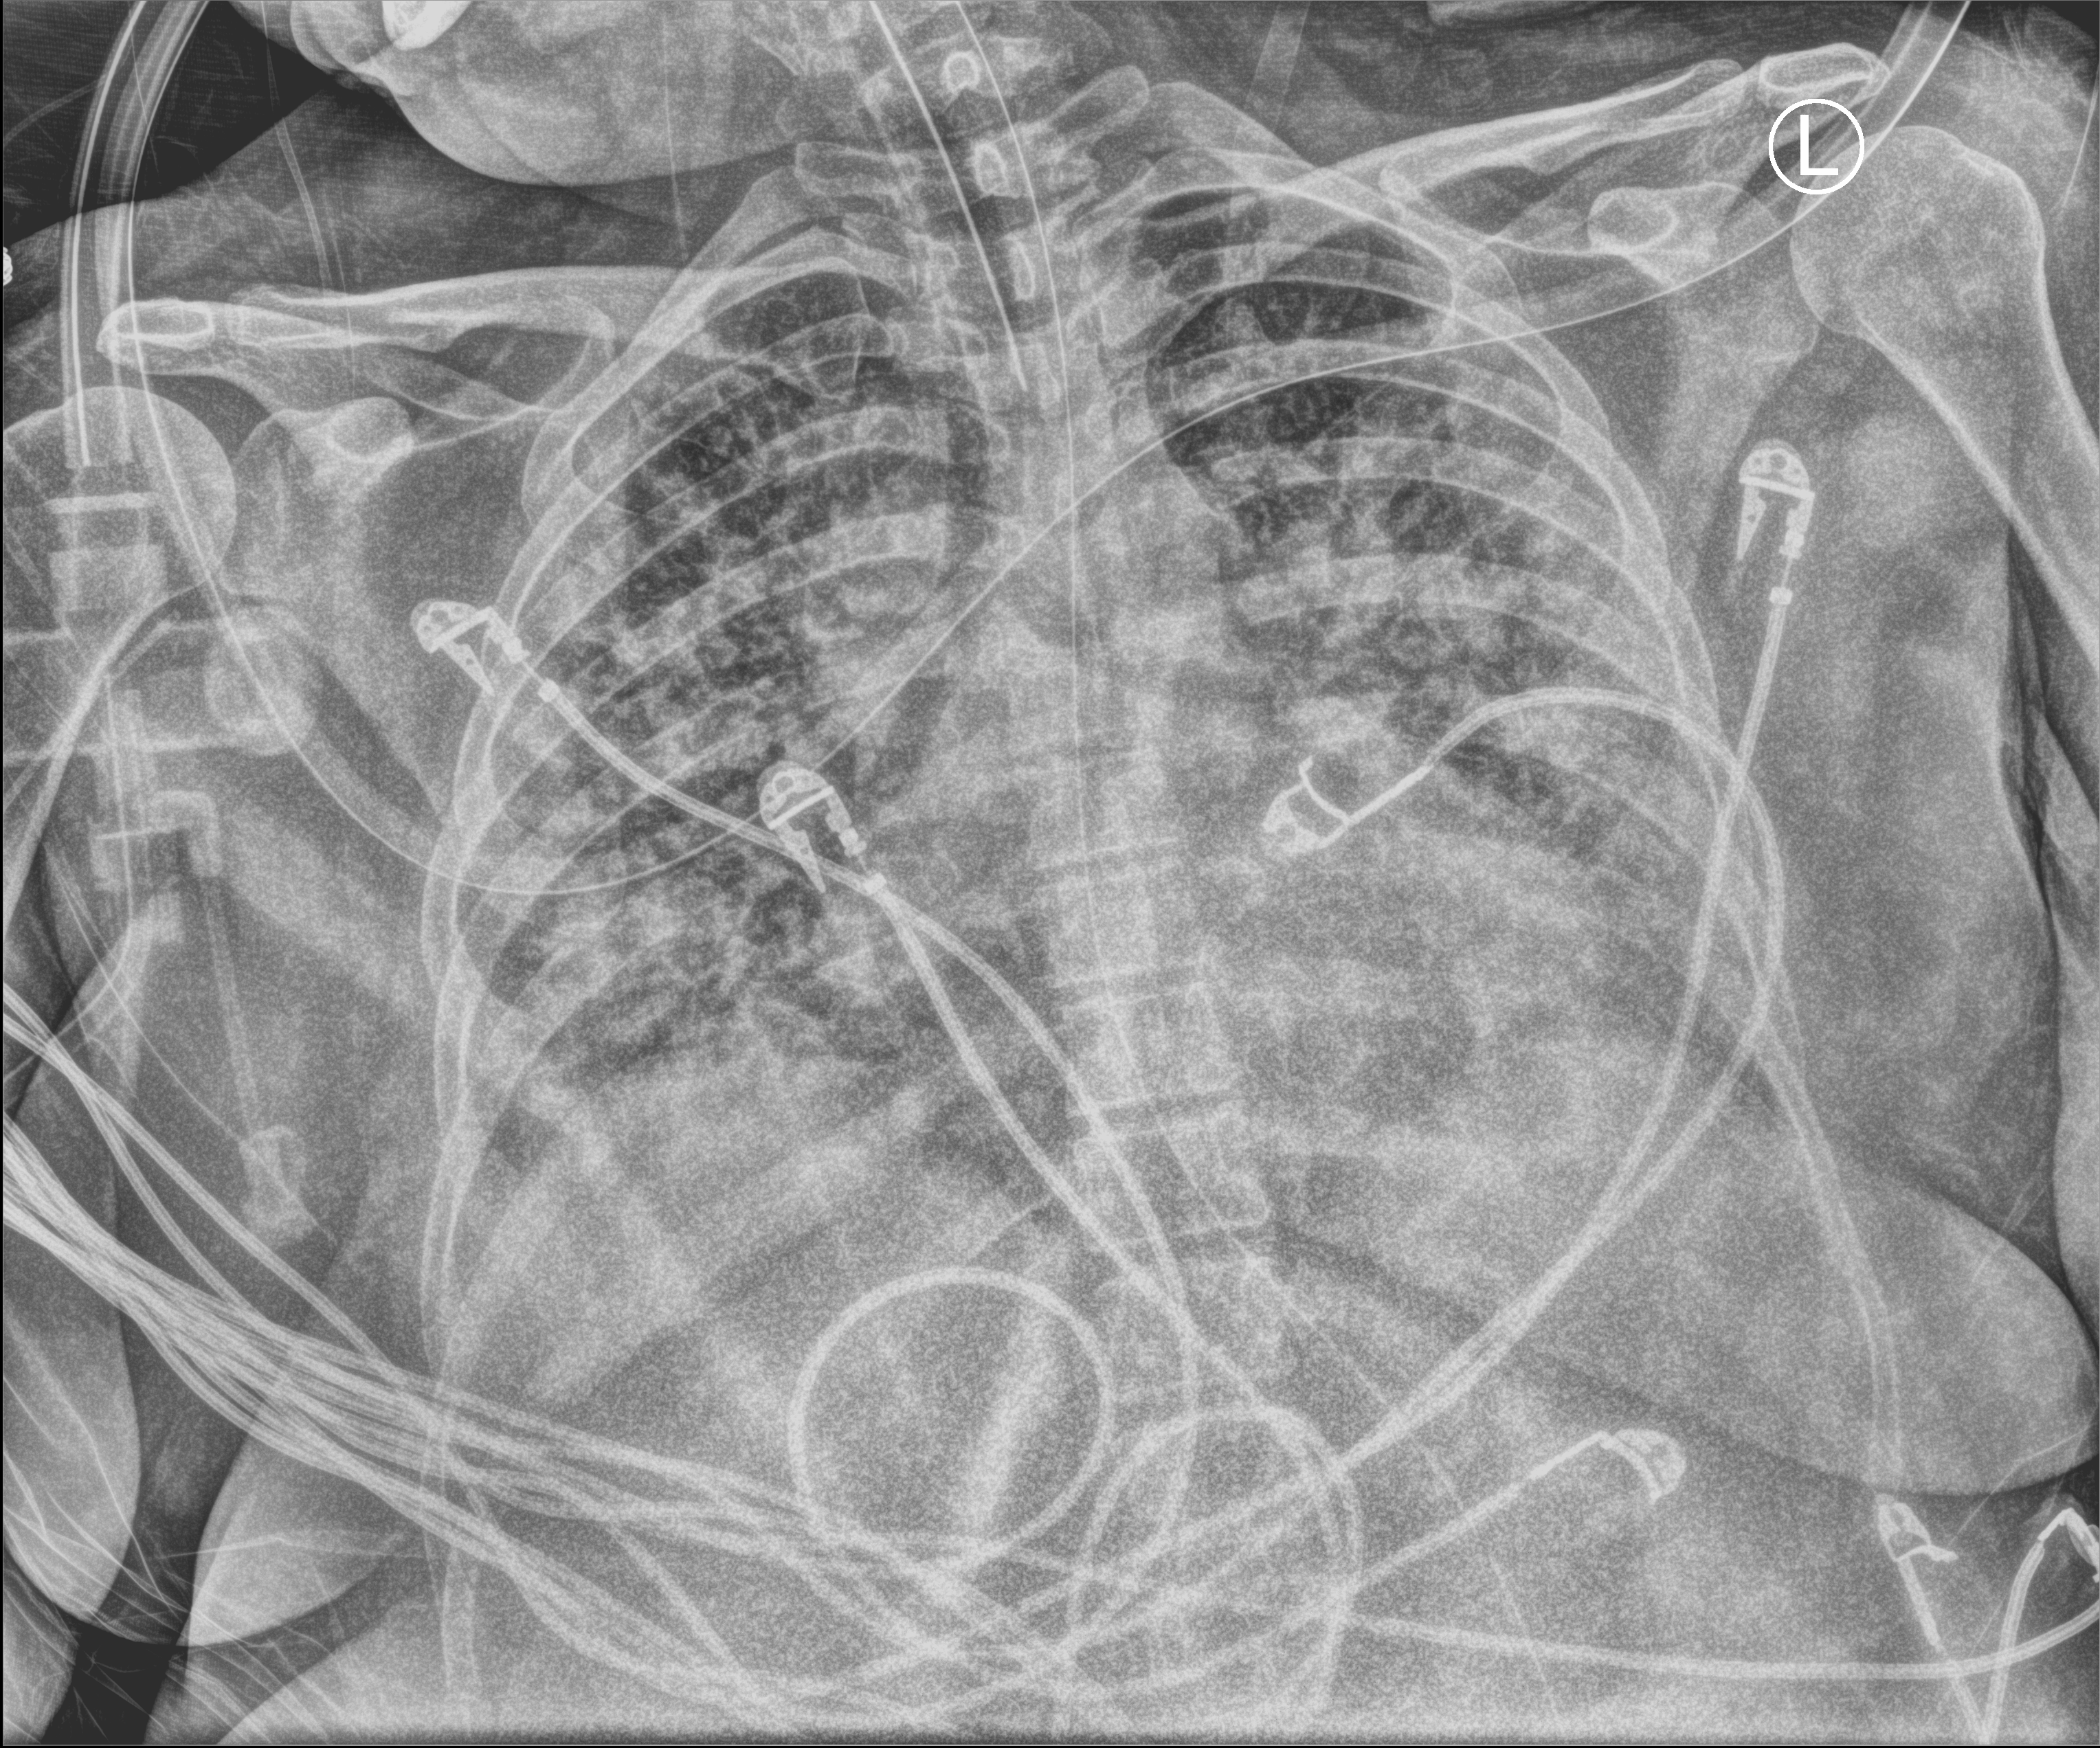
Portable chest radiograph, anteroposterior (AP) projection. Female patient hospitalised with COVID-19, age 18–59 years.
Admission-level facts for this patient (not findings on this image; timing relative to this image not recorded): mechanically ventilated during this hospital stay: yes; admitted to intensive care during this hospital stay: yes; length of hospital stay: 31 days.